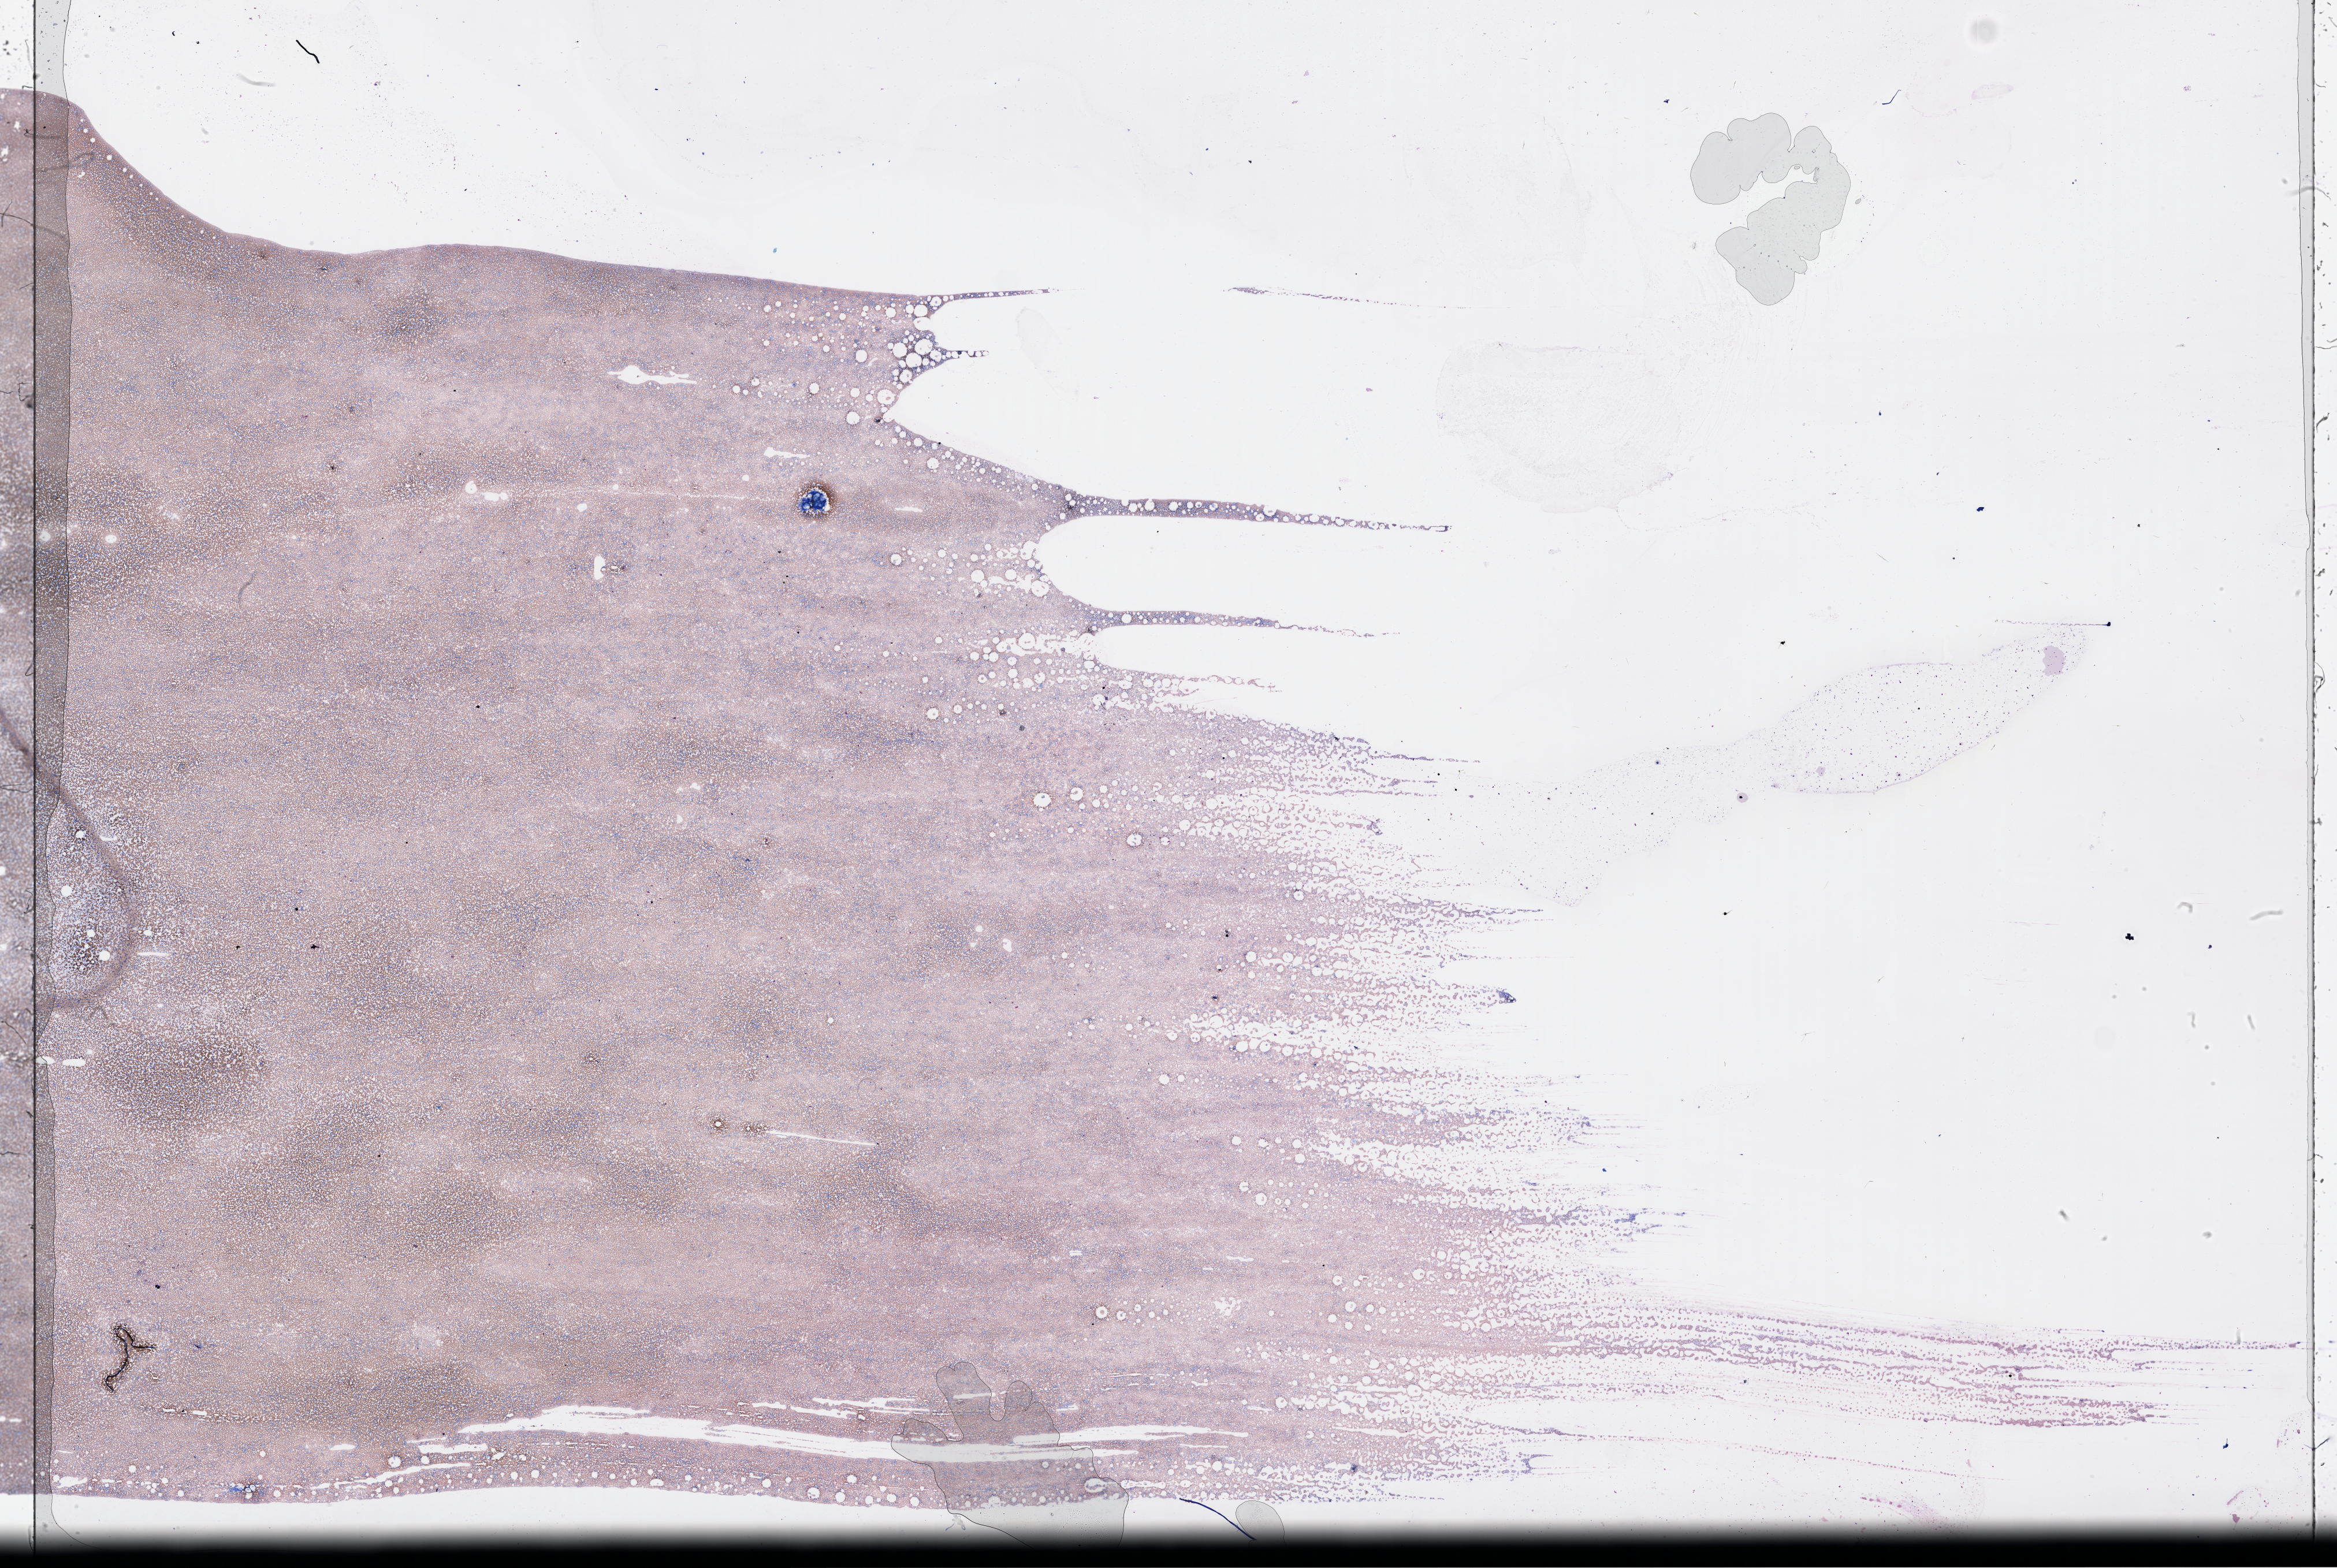
Hematoxylin and eosin (H&E) stained whole-slide image, shown as a low-resolution overview of the whole scanned area (about 32.7 x 21.9 mm), bone marrow (leukaemic) sample. Male, 69 y/o.
FAB classification: M2. Diagnosis: Acute Myeloid Leukemia.